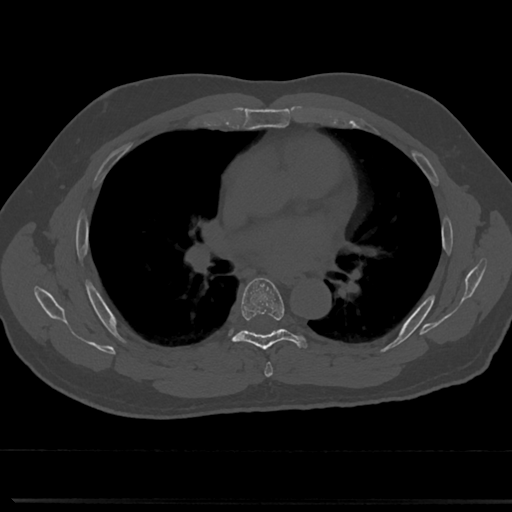
CT including the spine, one axial slice; position 454 of 817 along the scan axis; reconstruction kernel Br40s/3; 120 kVp; bone window (W 1800 / L 400 HU); 0.5 mm slice thickness; 512 × 512 image matrix, field of view 355 × 355 mm. Patient: male, 61 years. From the clinical record (not read from this slice): primary cancer: prostate.
Annotated regions visible in this slice (semi-automatically segmented with operator editing):
- T5 vertebra: bounding box <261,345,272,373> (left, top, right, bottom; pixels)
- T6 vertebra: <218,276,310,355>